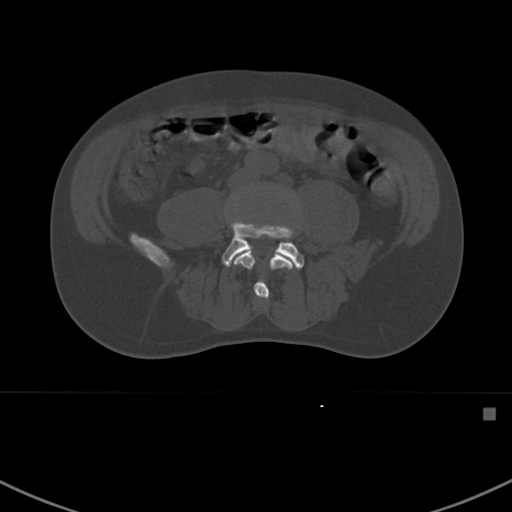
CT including the spine, one axial slice; reconstruction kernel Br40s; 120 kVp; bone window (W 1800 / L 400 HU); 1.5 mm slice thickness; 512 × 512 image matrix. Male patient, age 59 years. From the clinical record (not read from this slice): primary cancer: prostate.
Structures marked on this image (semi-automatically segmented with operator editing):
- L4 vertebra: bounding box [x1, y1, x2, y2] px = [233, 197, 297, 300]
- L5 vertebra: [221, 220, 304, 269]